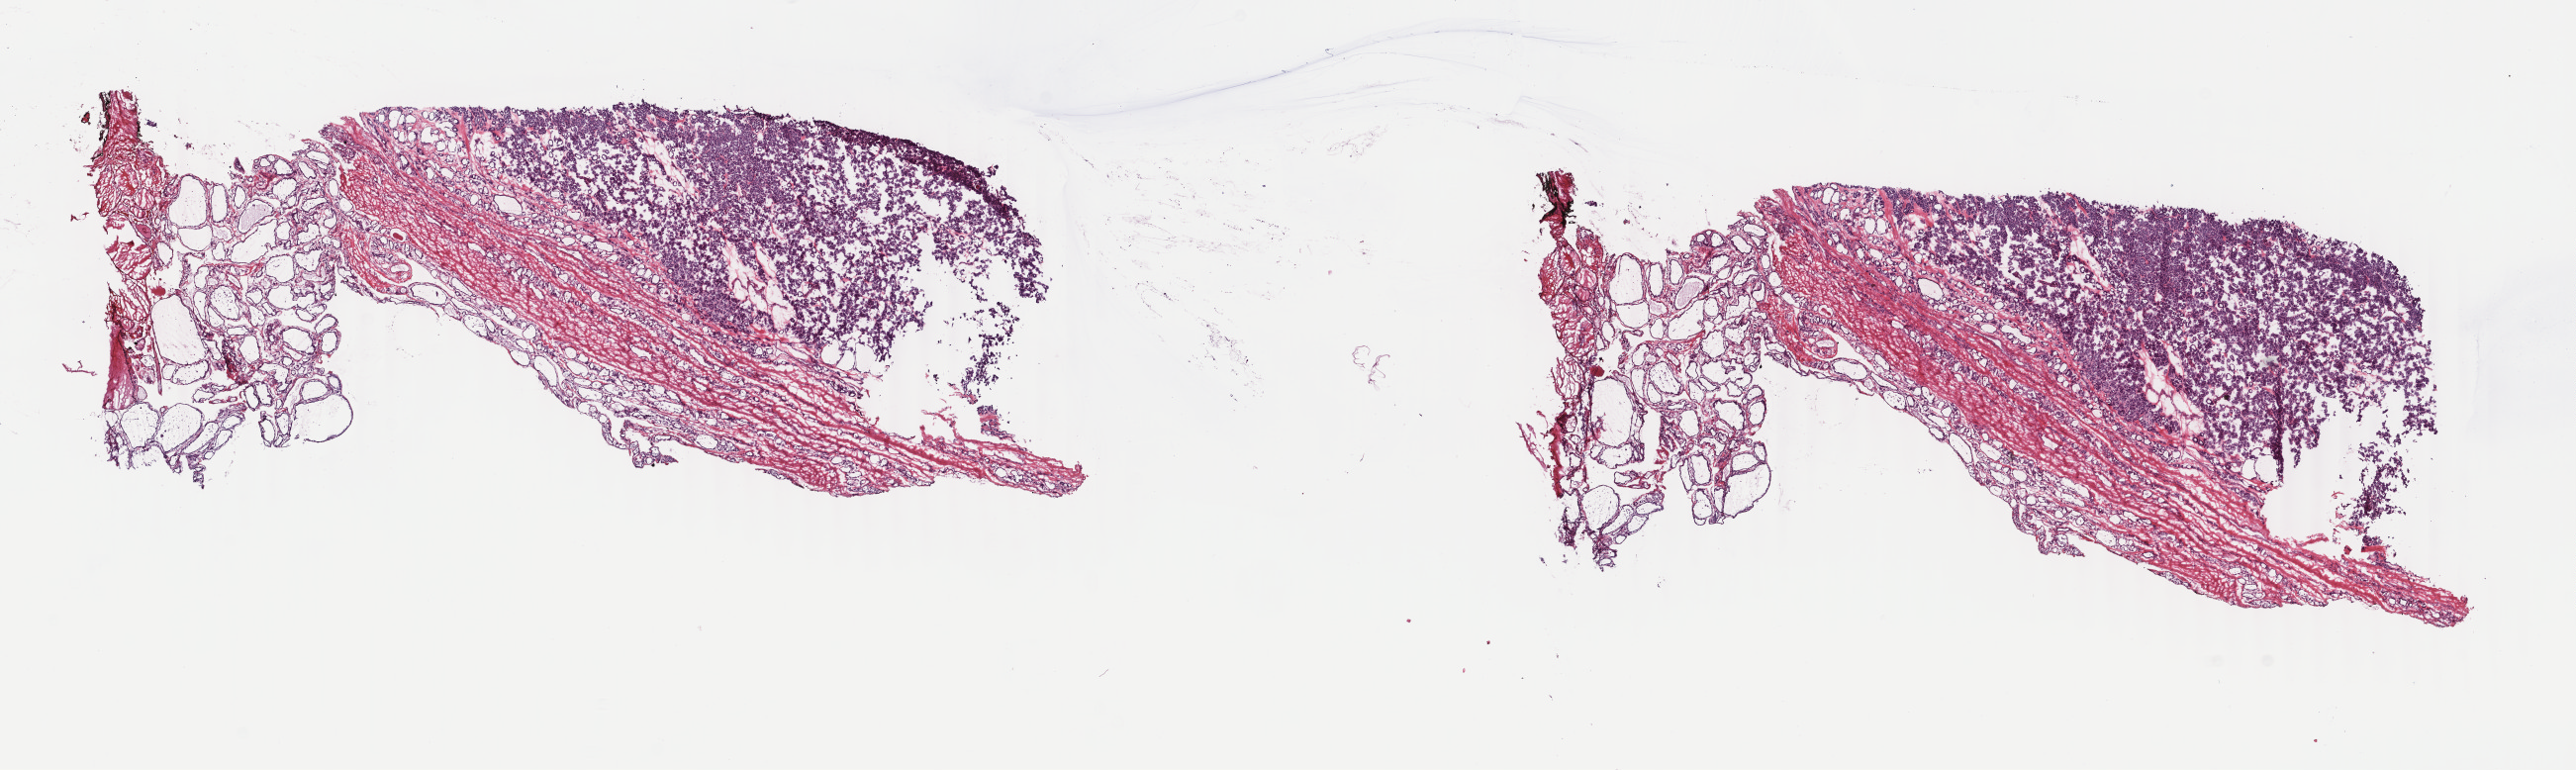
Digitized H&E tissue section (whole slide) — a low-resolution overview of the entire scanned area, about 20.7 x 6.2 mm (slide scanned at 40x), frozen section from the top of the tissue portion, thyroid, primary tumour sample. Female, age 45 years at initial diagnosis. Composition of this section per pathologist review: tumour cells 70%, tumour nuclei 70%, normal cells 3%, stromal cells 27%, necrosis 0%. Inflammatory infiltration, as recorded: lymphocyte infiltration 3%, monocyte infiltration 1%, neutrophil infiltration 1%.
Histologic diagnosis: Papillary carcinoma, follicular variant (thyroid gland). AJCC pathologic stage: II. Laterality: right.